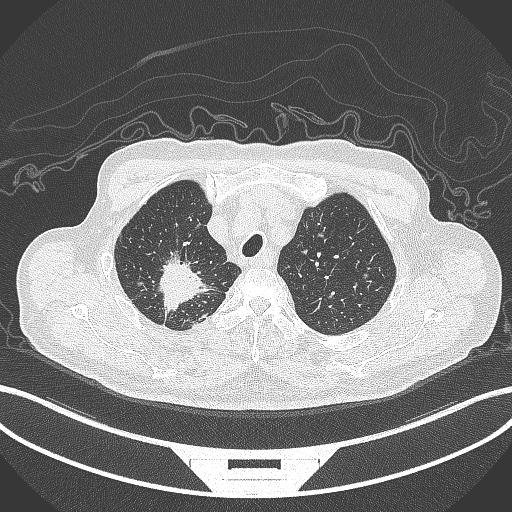
Chest CT, one axial slice. Position 318 of 407 along the scan axis. Lung window (W 1500 / L -600 HU). 512 × 512 image matrix, field of view 400 × 400 mm. Patient: male, 69 years. Case-level facts recorded for this patient, not image findings: clinical TNM (as recorded): T1c N1 M1.
Annotated regions visible in this slice (bounding box drawn by a radiologist):
- lung tumour (recorded histology: adenocarcinoma): bounding box [x1, y1, x2, y2] px = [148, 247, 216, 315]